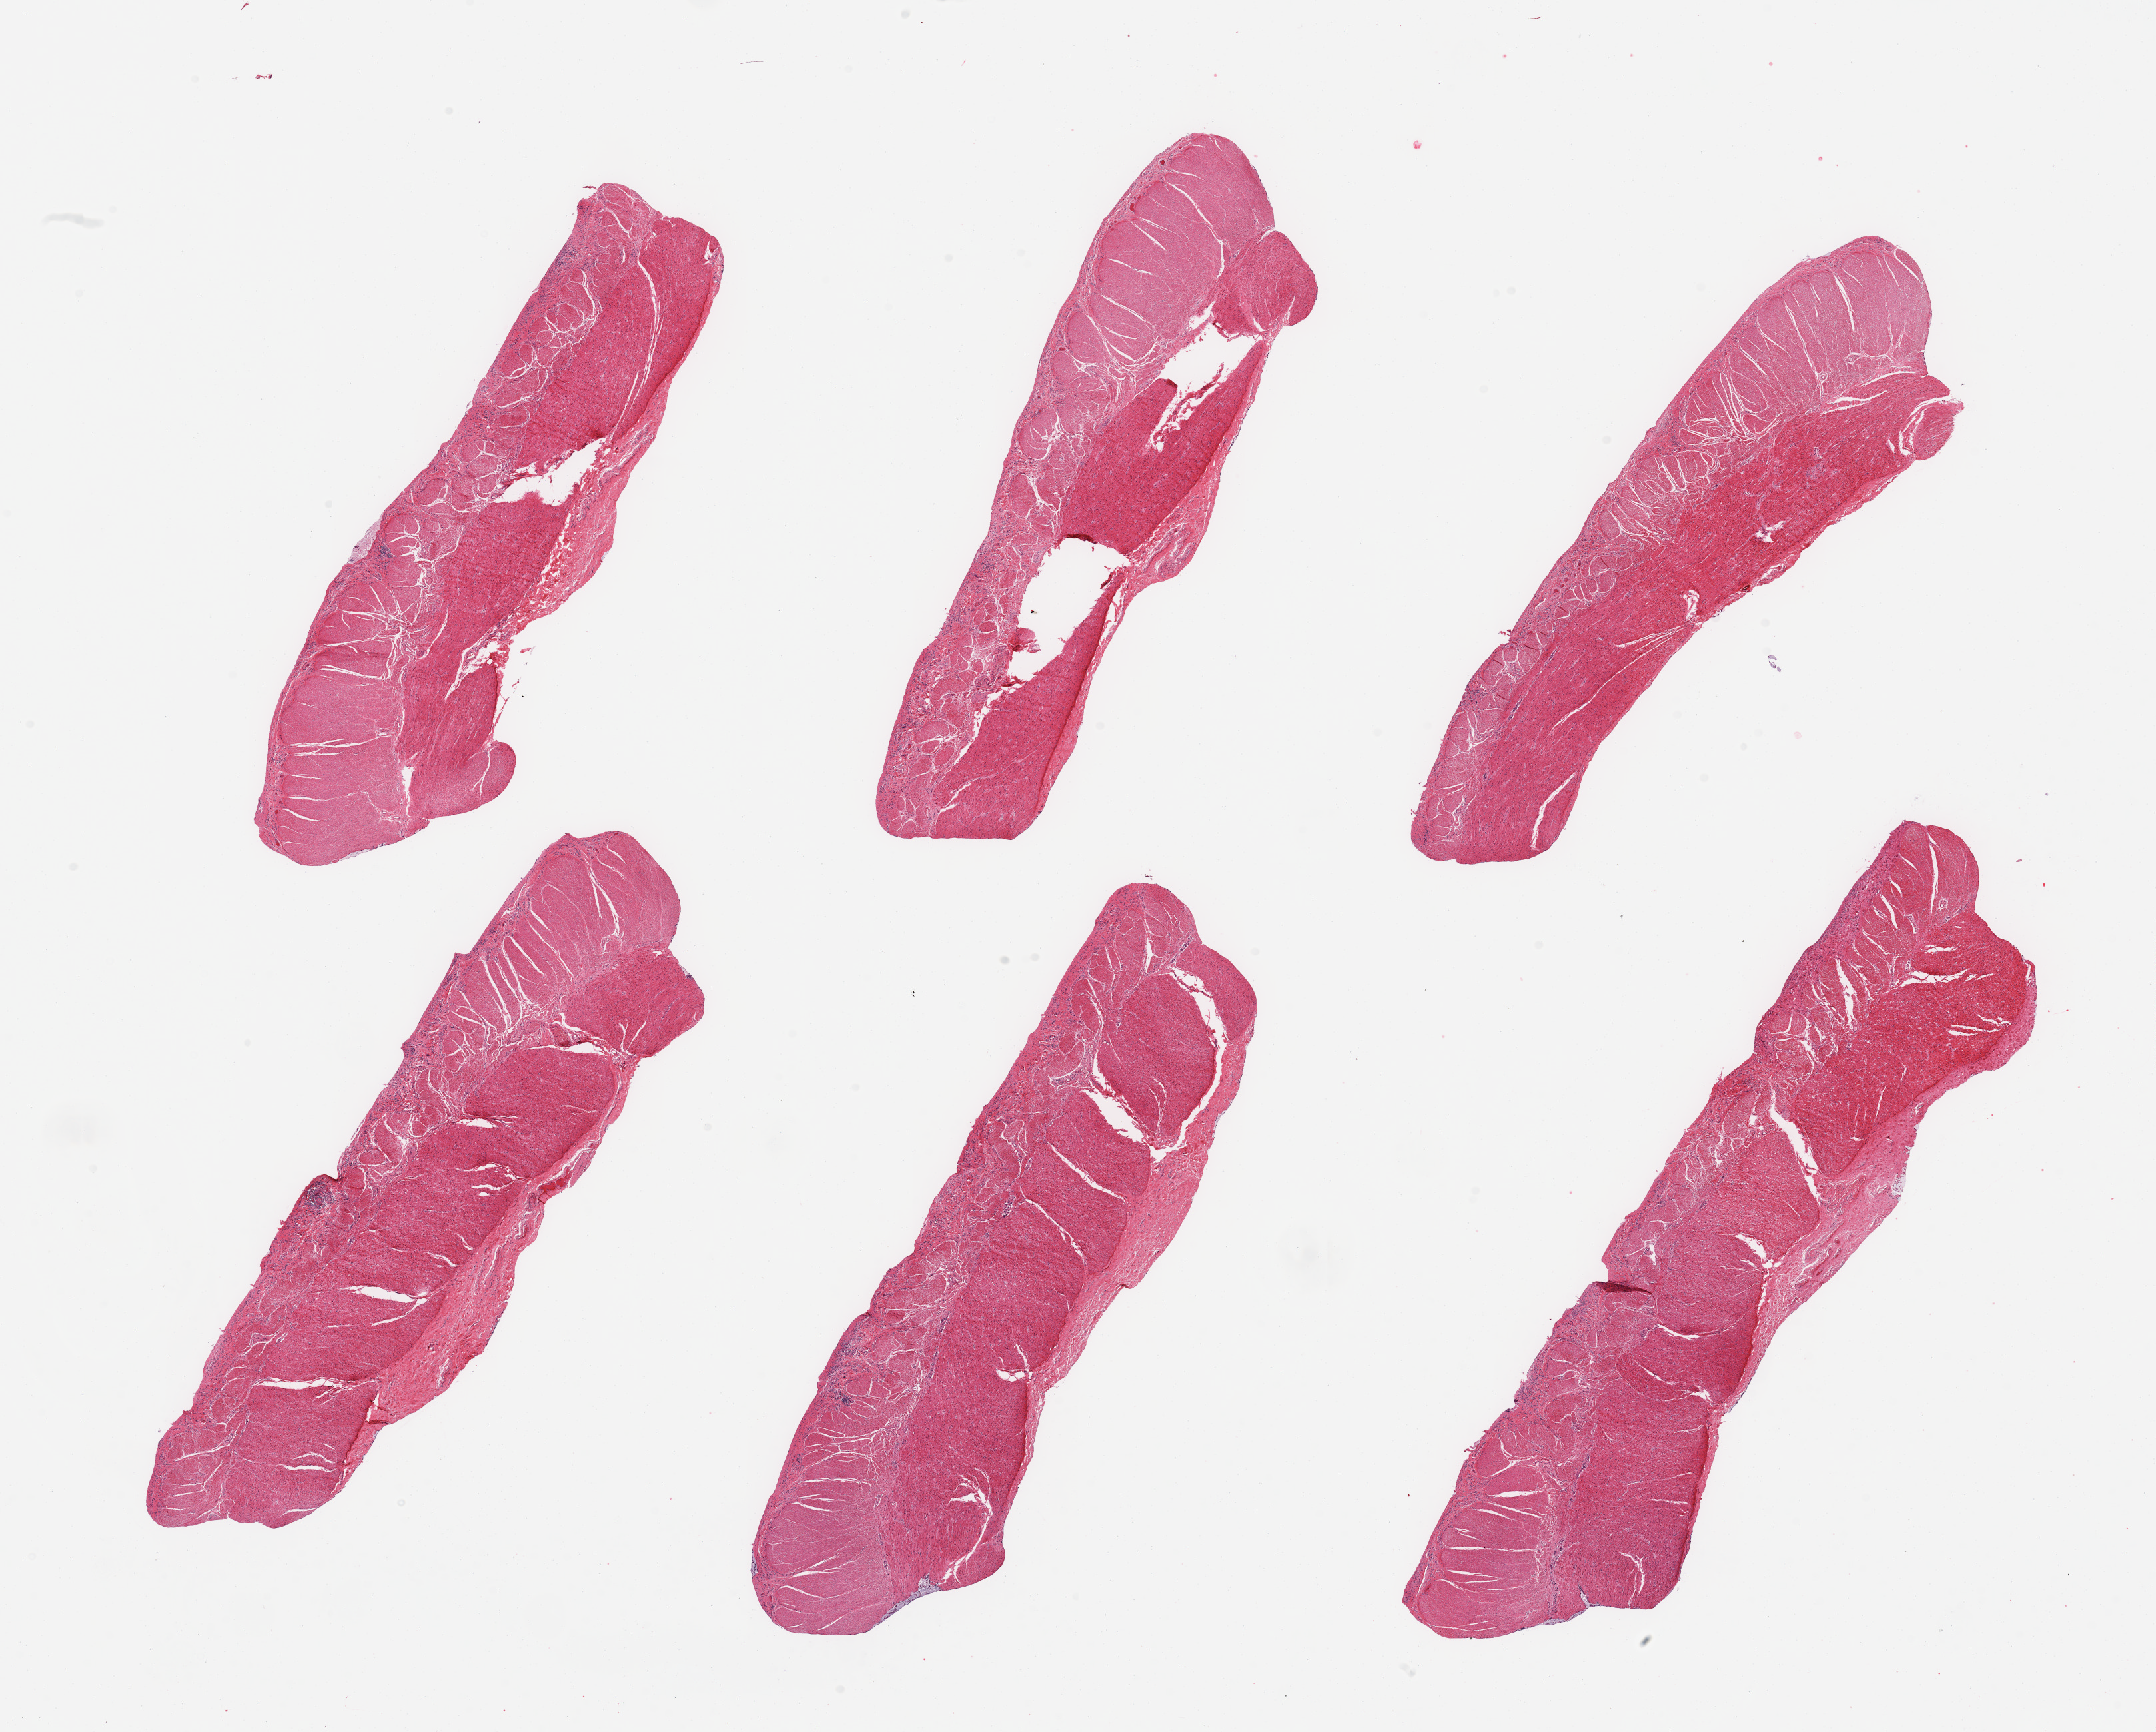
Digitized haematoxylin and eosin-stained section, a low-resolution overview of the entire scanned area, about 25.6 x 20.6 mm. PAXgene-fixed, paraffin-embedded tissue. Sampled site (target tissue): sigmoid colon. Donor tissue sample. Donor: male.
Pathologist's review note for this sample: 6 pieces, confirmed target muscularis.